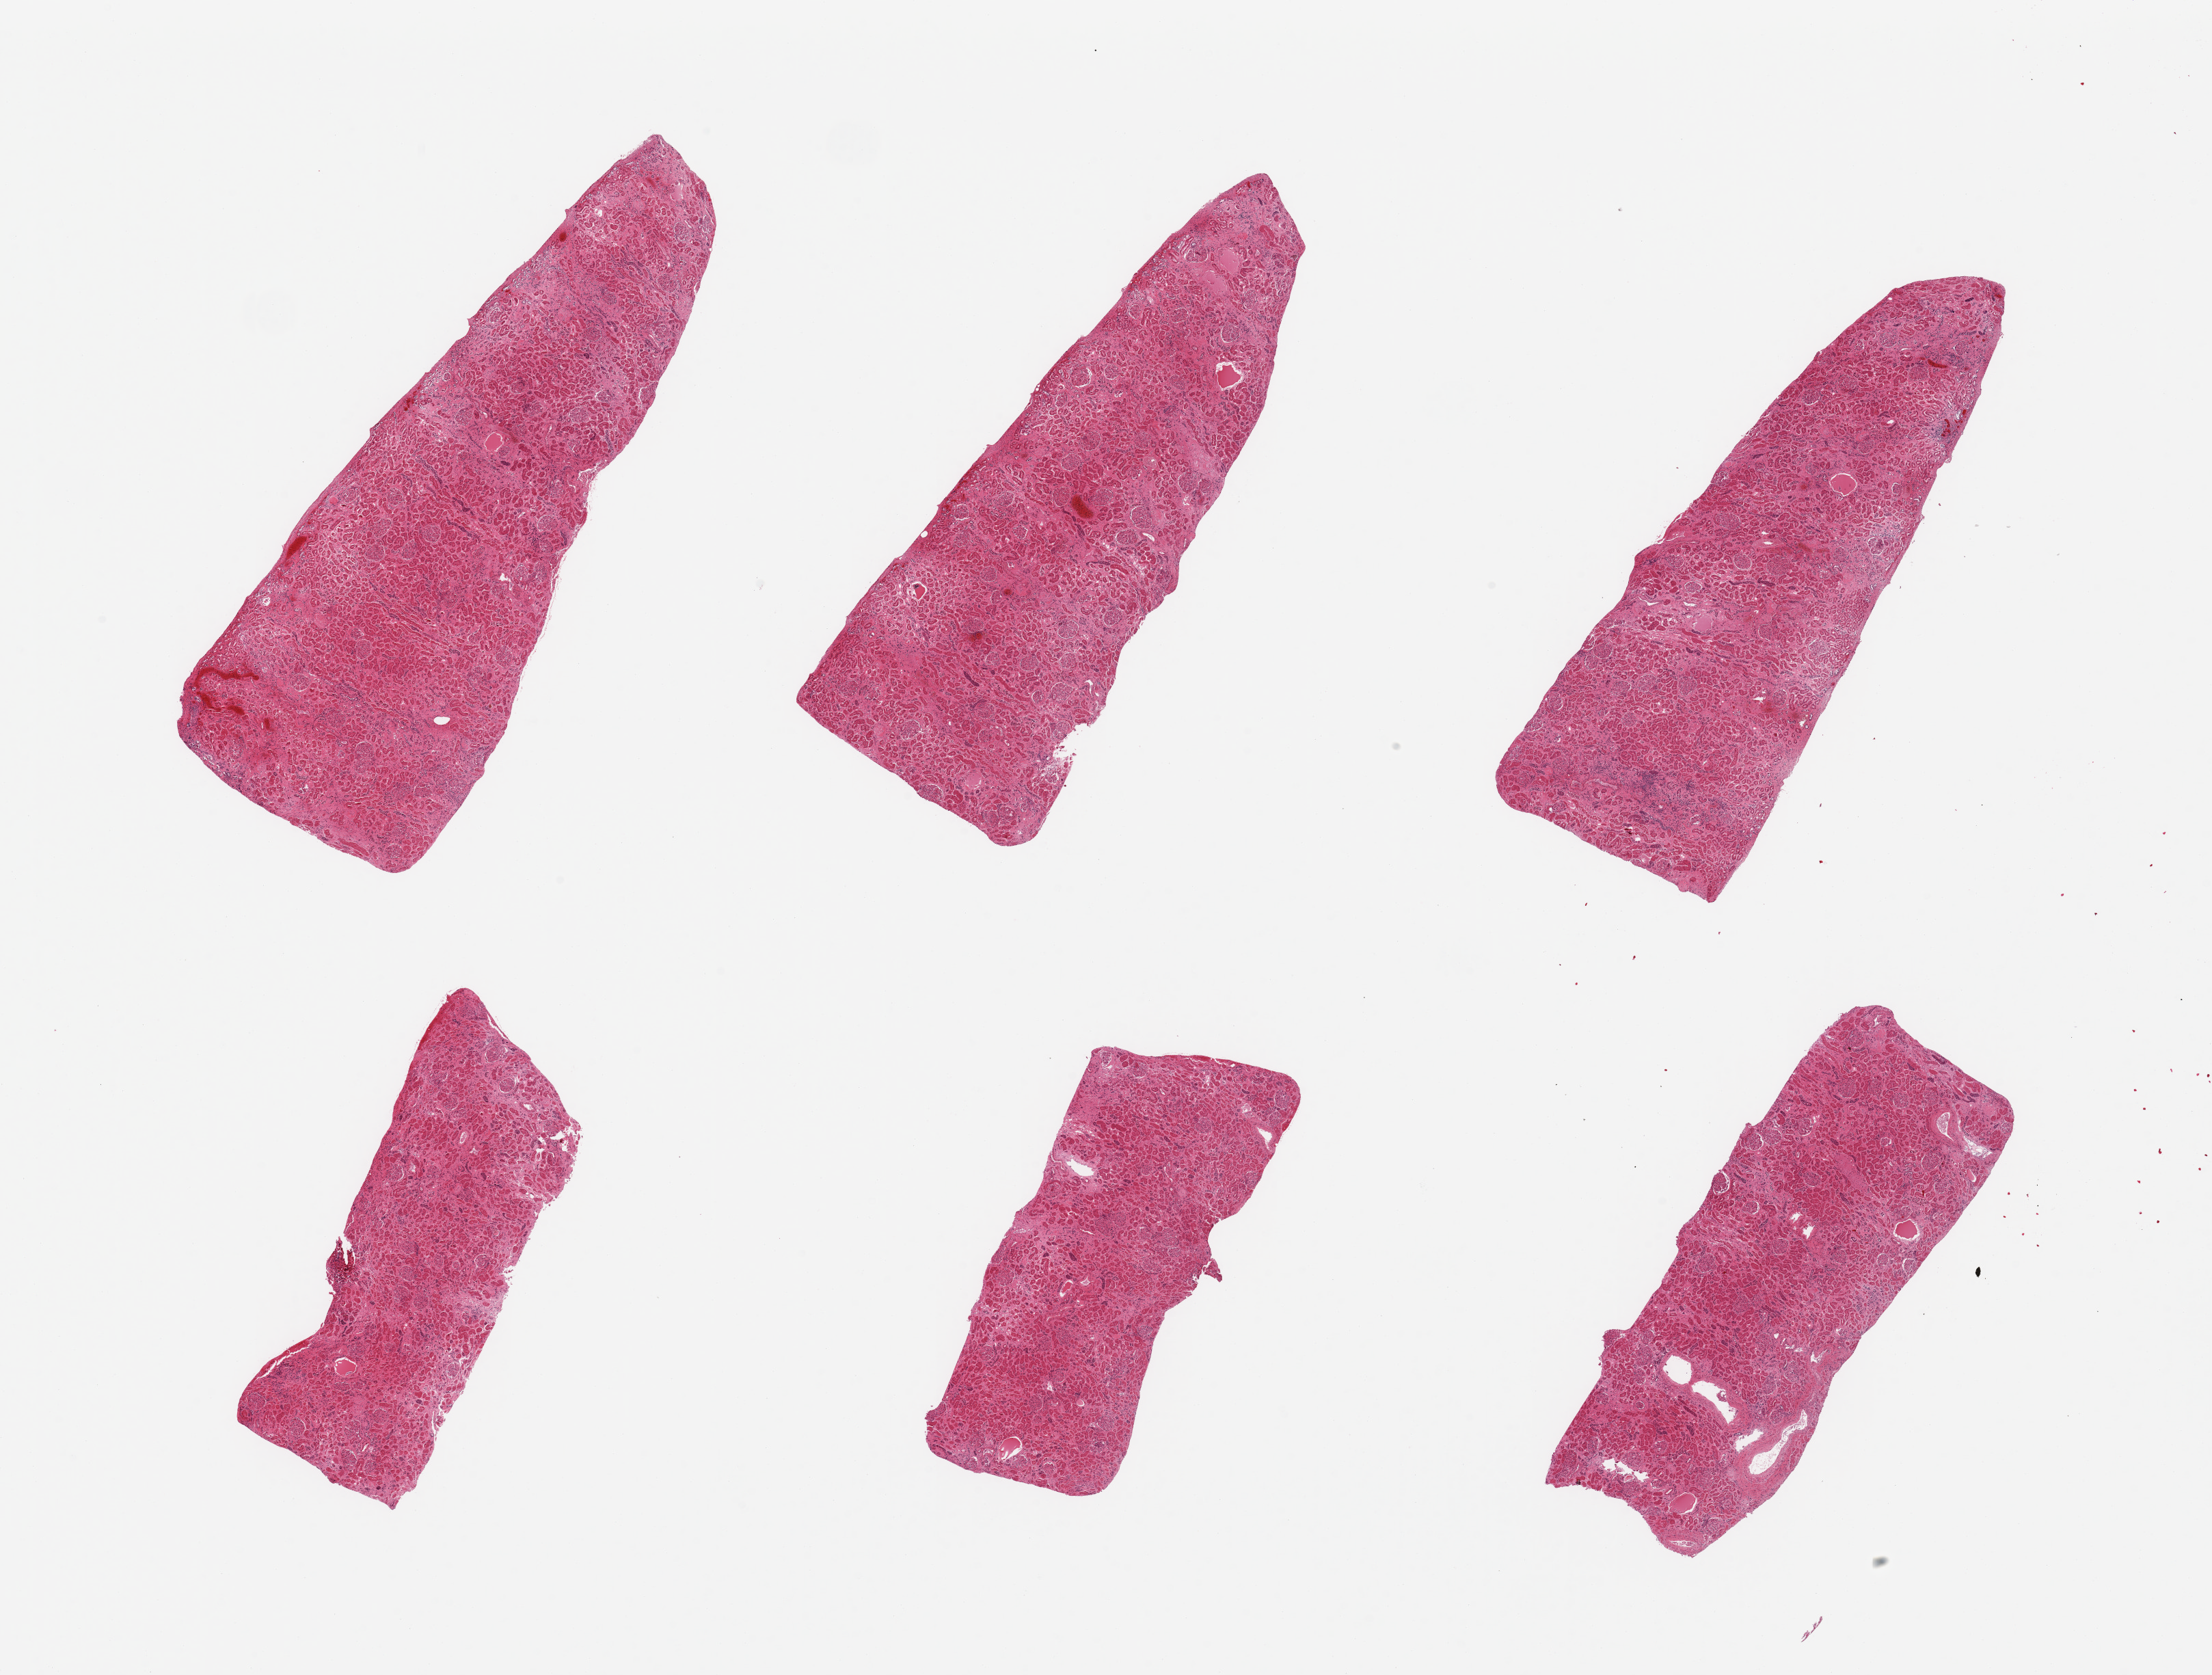
Digitized H&E-stained section, shown as a low-resolution overview of the whole scanned area (about 25.6 x 19.4 mm, slide scanned at 20x), PAXgene-fixed paraffin-embedded (PFPE) section, target tissue: renal cortex, tissue donor sample. Donor sex: male.
Reviewer comment on this tissue sample: 6 pieces; moderately to severely autolyzed tubules; scattered hyalinized glomeruli, interstitial fibrosis and focal chronic inflammation suggestive of chronic glomerulonephritis.